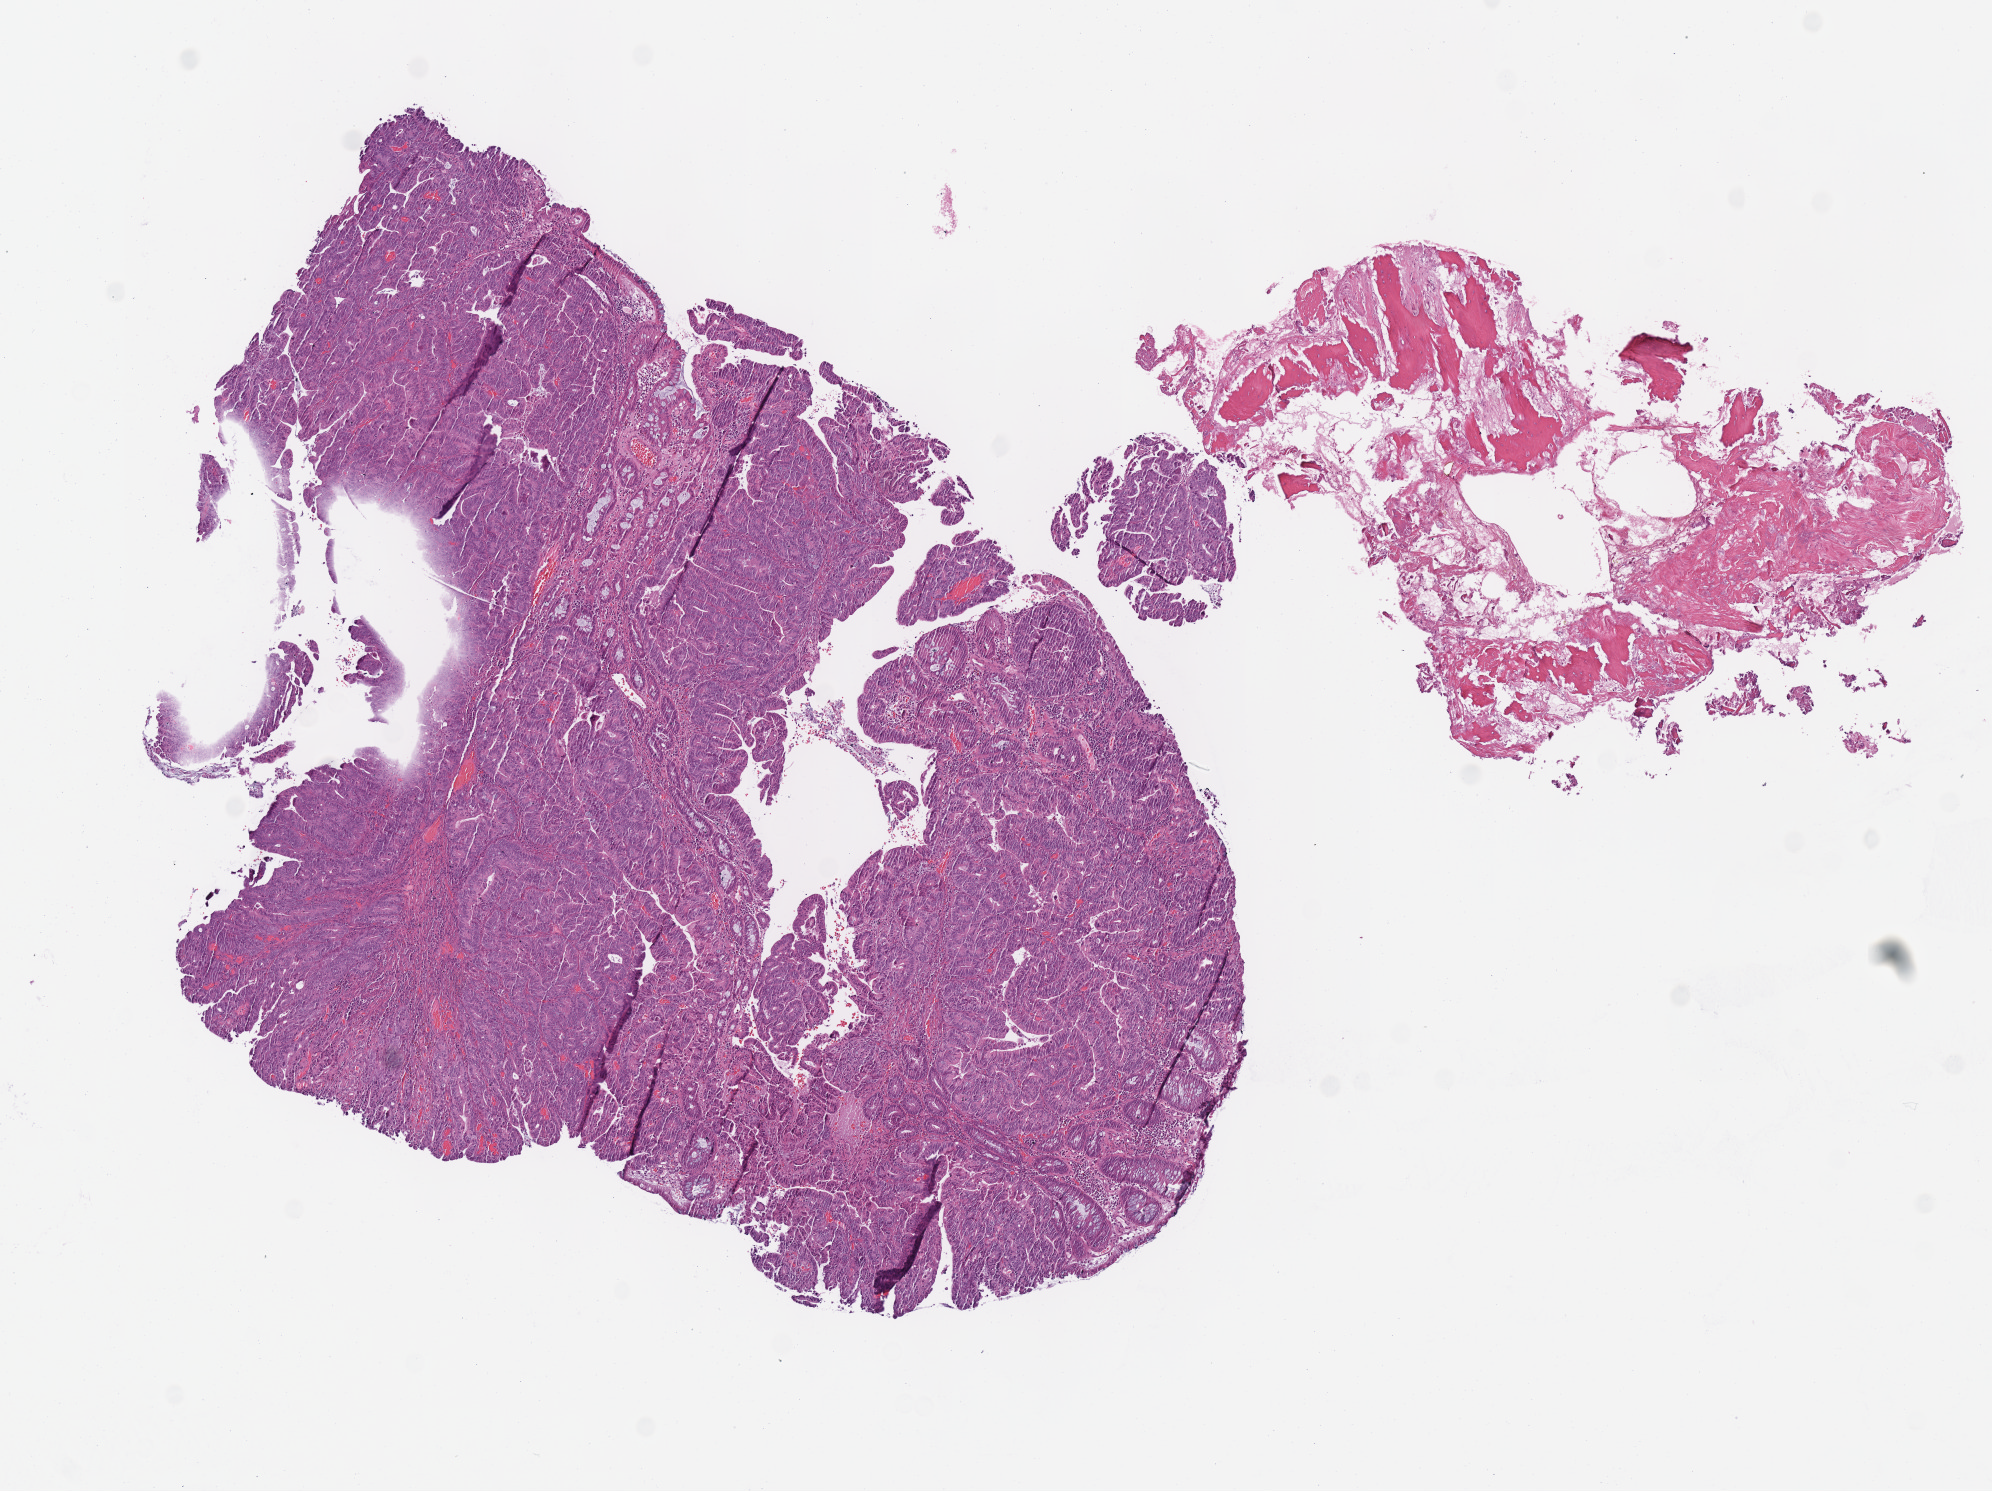
H&E-stained whole-slide image — whole scanned area (about 7.8 x 5.9 mm, from a 40x scan) shown as a low-resolution overview; frozen section from the top of the tissue portion; sample: primary tumour, colon. Female, age 43 years at initial diagnosis. Composition of this section per pathologist review: tumour cells 70%, tumour nuclei 80%, normal cells 20%, stromal cells 5%, necrosis 5%.
• AJCC pathologic stage: IIIB
• diagnosis: Adenocarcinoma, NOS (transverse colon)
• lymph nodes positive (case pathology): 2 of 26 examined